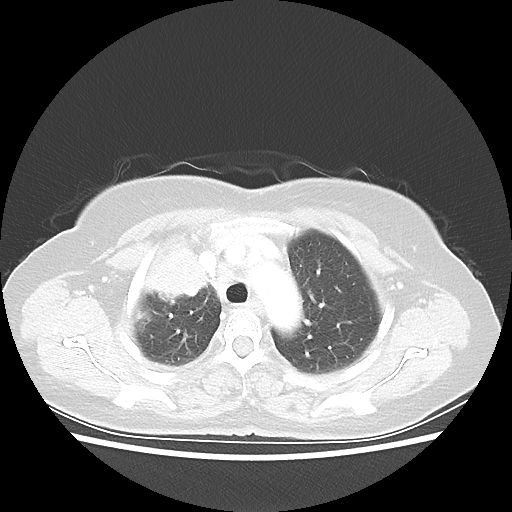
Chest CT, one axial slice. Position 42 of 55 along the scan axis. 80 kVp. Lung window (W 1500 / L -600 HU). 512 × 512 image matrix, field of view 337 × 337 mm. Female patient, age 62 years. From the clinical record (not read from this slice): clinical TNM (as recorded): T4 N3 M0.
Annotated regions visible in this slice (bounding box drawn by a radiologist):
- lung tumour (recorded histology: squamous cell carcinoma): box from (x=142, y=240) to (x=216, y=304) px